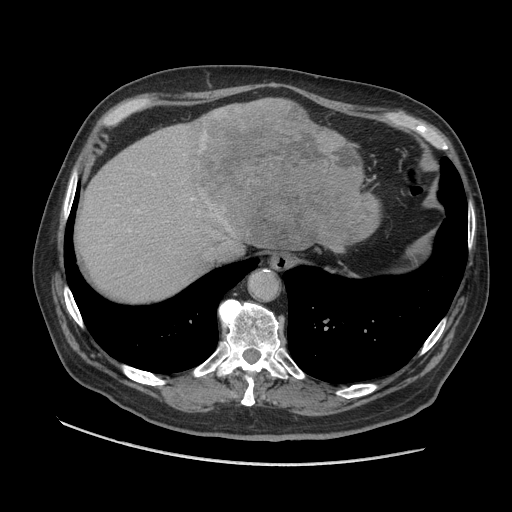
Contrast-enhanced abdominal CT (liver protocol), one axial slice; position 80 of 109 along the scan axis; soft-tissue window (W 400 / L 40 HU); 512 × 512 image matrix, field of view 420 × 420 mm. From the clinical record (not read from this slice): diagnosis: hepatocellular carcinoma (patient treated with transarterial chemoembolisation; whether this scan precedes or follows treatment is not stated here); TNM stage (as recorded): Stage-I; Child-Pugh class: A; tumour nodularity: uninodular.
Outlined on this slice (semi-automatically segmented with operator editing):
- liver parenchyma outside the tumour (the mass and vessels are separate outlines, so this box may not span the whole liver): box from (x=76, y=106) to (x=372, y=300) px
- mass: (x=188, y=97)–(x=381, y=253)
- liver vessels: (x=128, y=199)–(x=193, y=232)